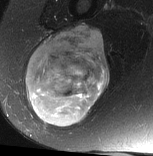
MRI of an extremity soft-tissue mass, one axial slice; position 36 of 77 along the scan axis; T2-weighted fat-saturated; MR volume resampled by the dataset authors to the PET/CT grid (not the native acquisition matrix); 3.27 mm slice thickness; 153 × 156 image matrix, field of view 149 × 152 mm. Female patient. From the clinical record (not read from this slice): histological type: synovial sarcoma; grade: intermediate; site of the primary tumour: right buttock.
Outlined on this slice (expert contour drawn on MRI and transferred to this co-registered scan by the dataset authors):
- gross tumour volume including surrounding oedema: bounding box (x1, y1, x2, y2) in pixels: (26, 26, 111, 128)
- gross tumour volume (mass): (26, 26, 111, 128)